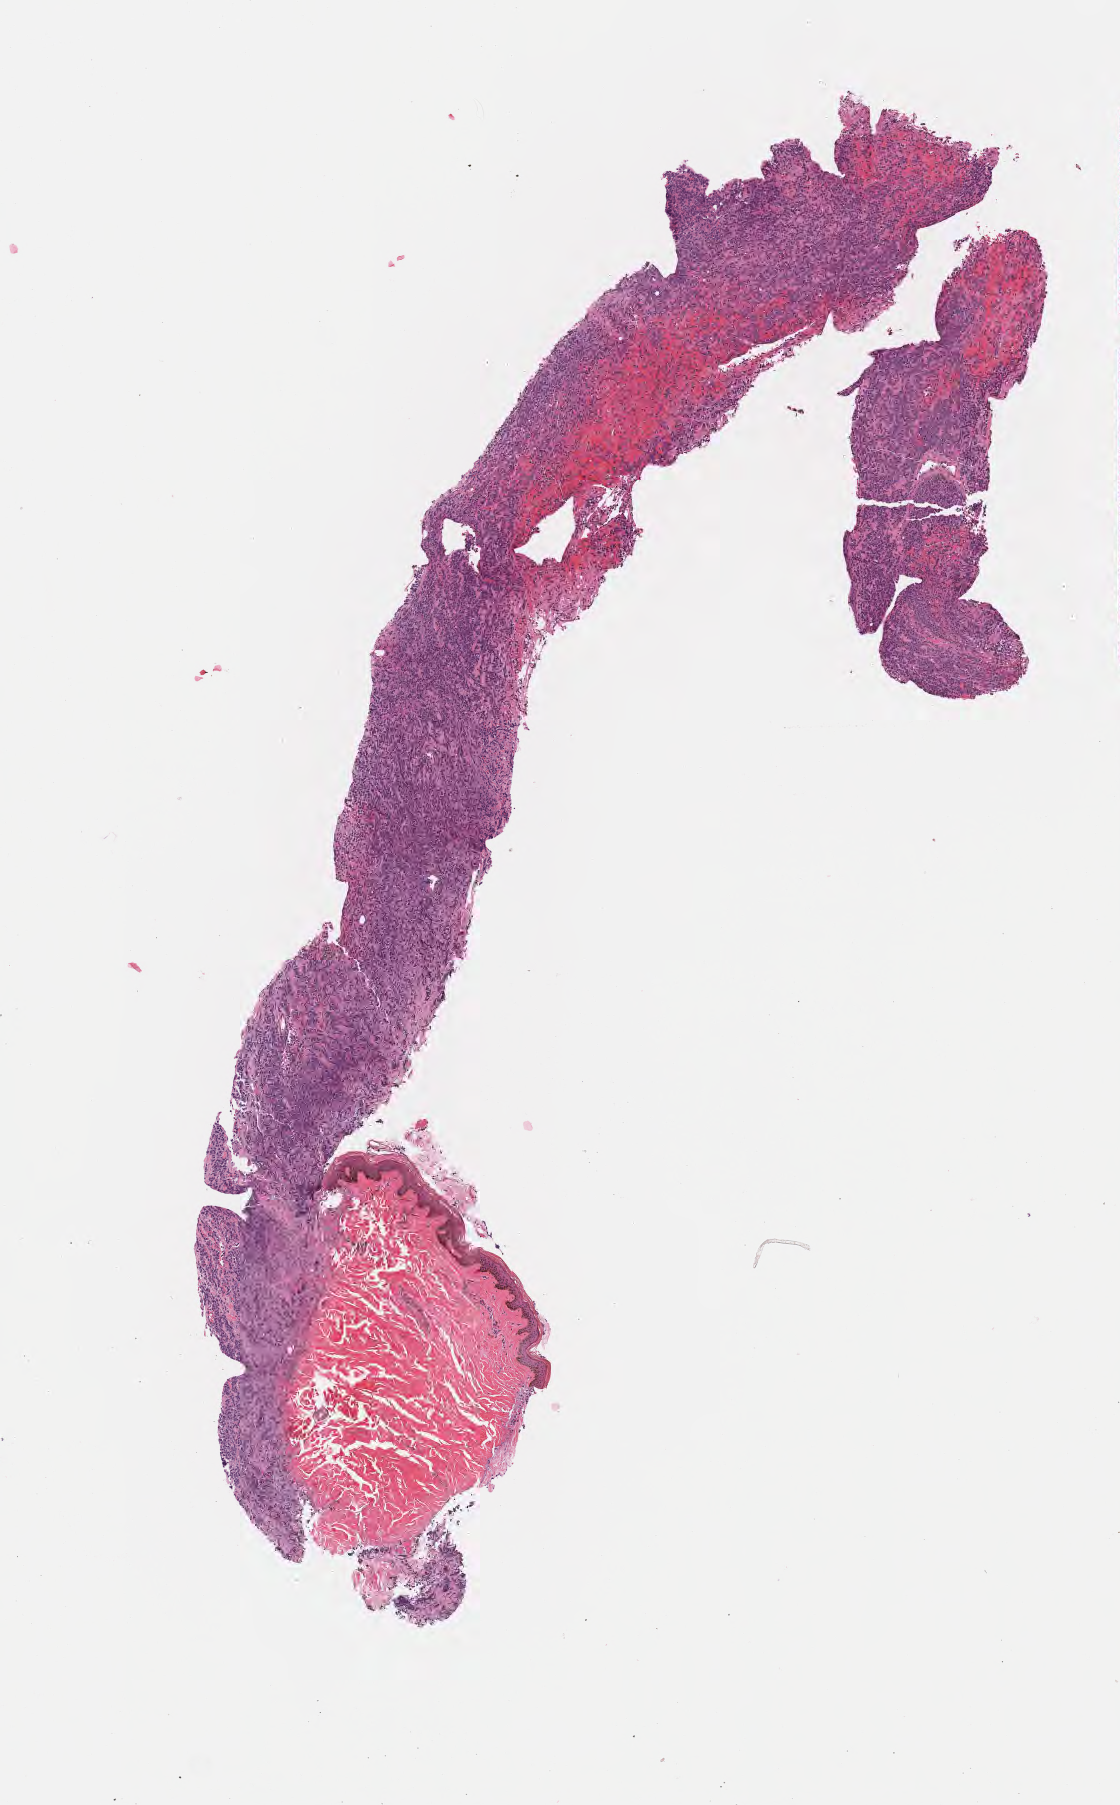
Whole-slide image, H&E stain — low-resolution overview of the scanned area, about 4.5 x 7.3 mm, specimen: tumor tissue. Patient: female, 43 years old.
- histologic diagnosis: Diffuse large B-cell lymphoma, NOS